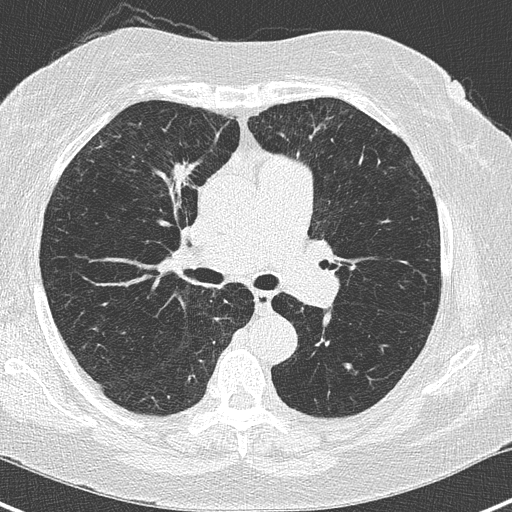
Low-dose screening chest CT, axial slice. Third annual screen. Lung window (W 1500 / L -600 HU). Lung (sharp) reconstruction kernel (B50f). 120 kVp. 512 × 512 image matrix, field of view 303 × 303 mm. Female participant, aged 62 years at enrolment. Current smoker at enrolment.
Expert-annotated lung lesion, bounding box <147,150,211,207> (left, top, right, bottom; pixels). The screening reader recorded 4 non-calcified nodules or masses ≥4 mm on this exam (right upper lobe, left lower lobe, left lower lobe); which of them this box marks is not recorded. Official screen result: positive, other. Participant outcome: lung cancer diagnosed 41 days after this screen — adenocarcinoma, NOS, right upper lobe, moderately differentiated (G2), stage IA (AJCC 6th edition), 15 mm at pathology.